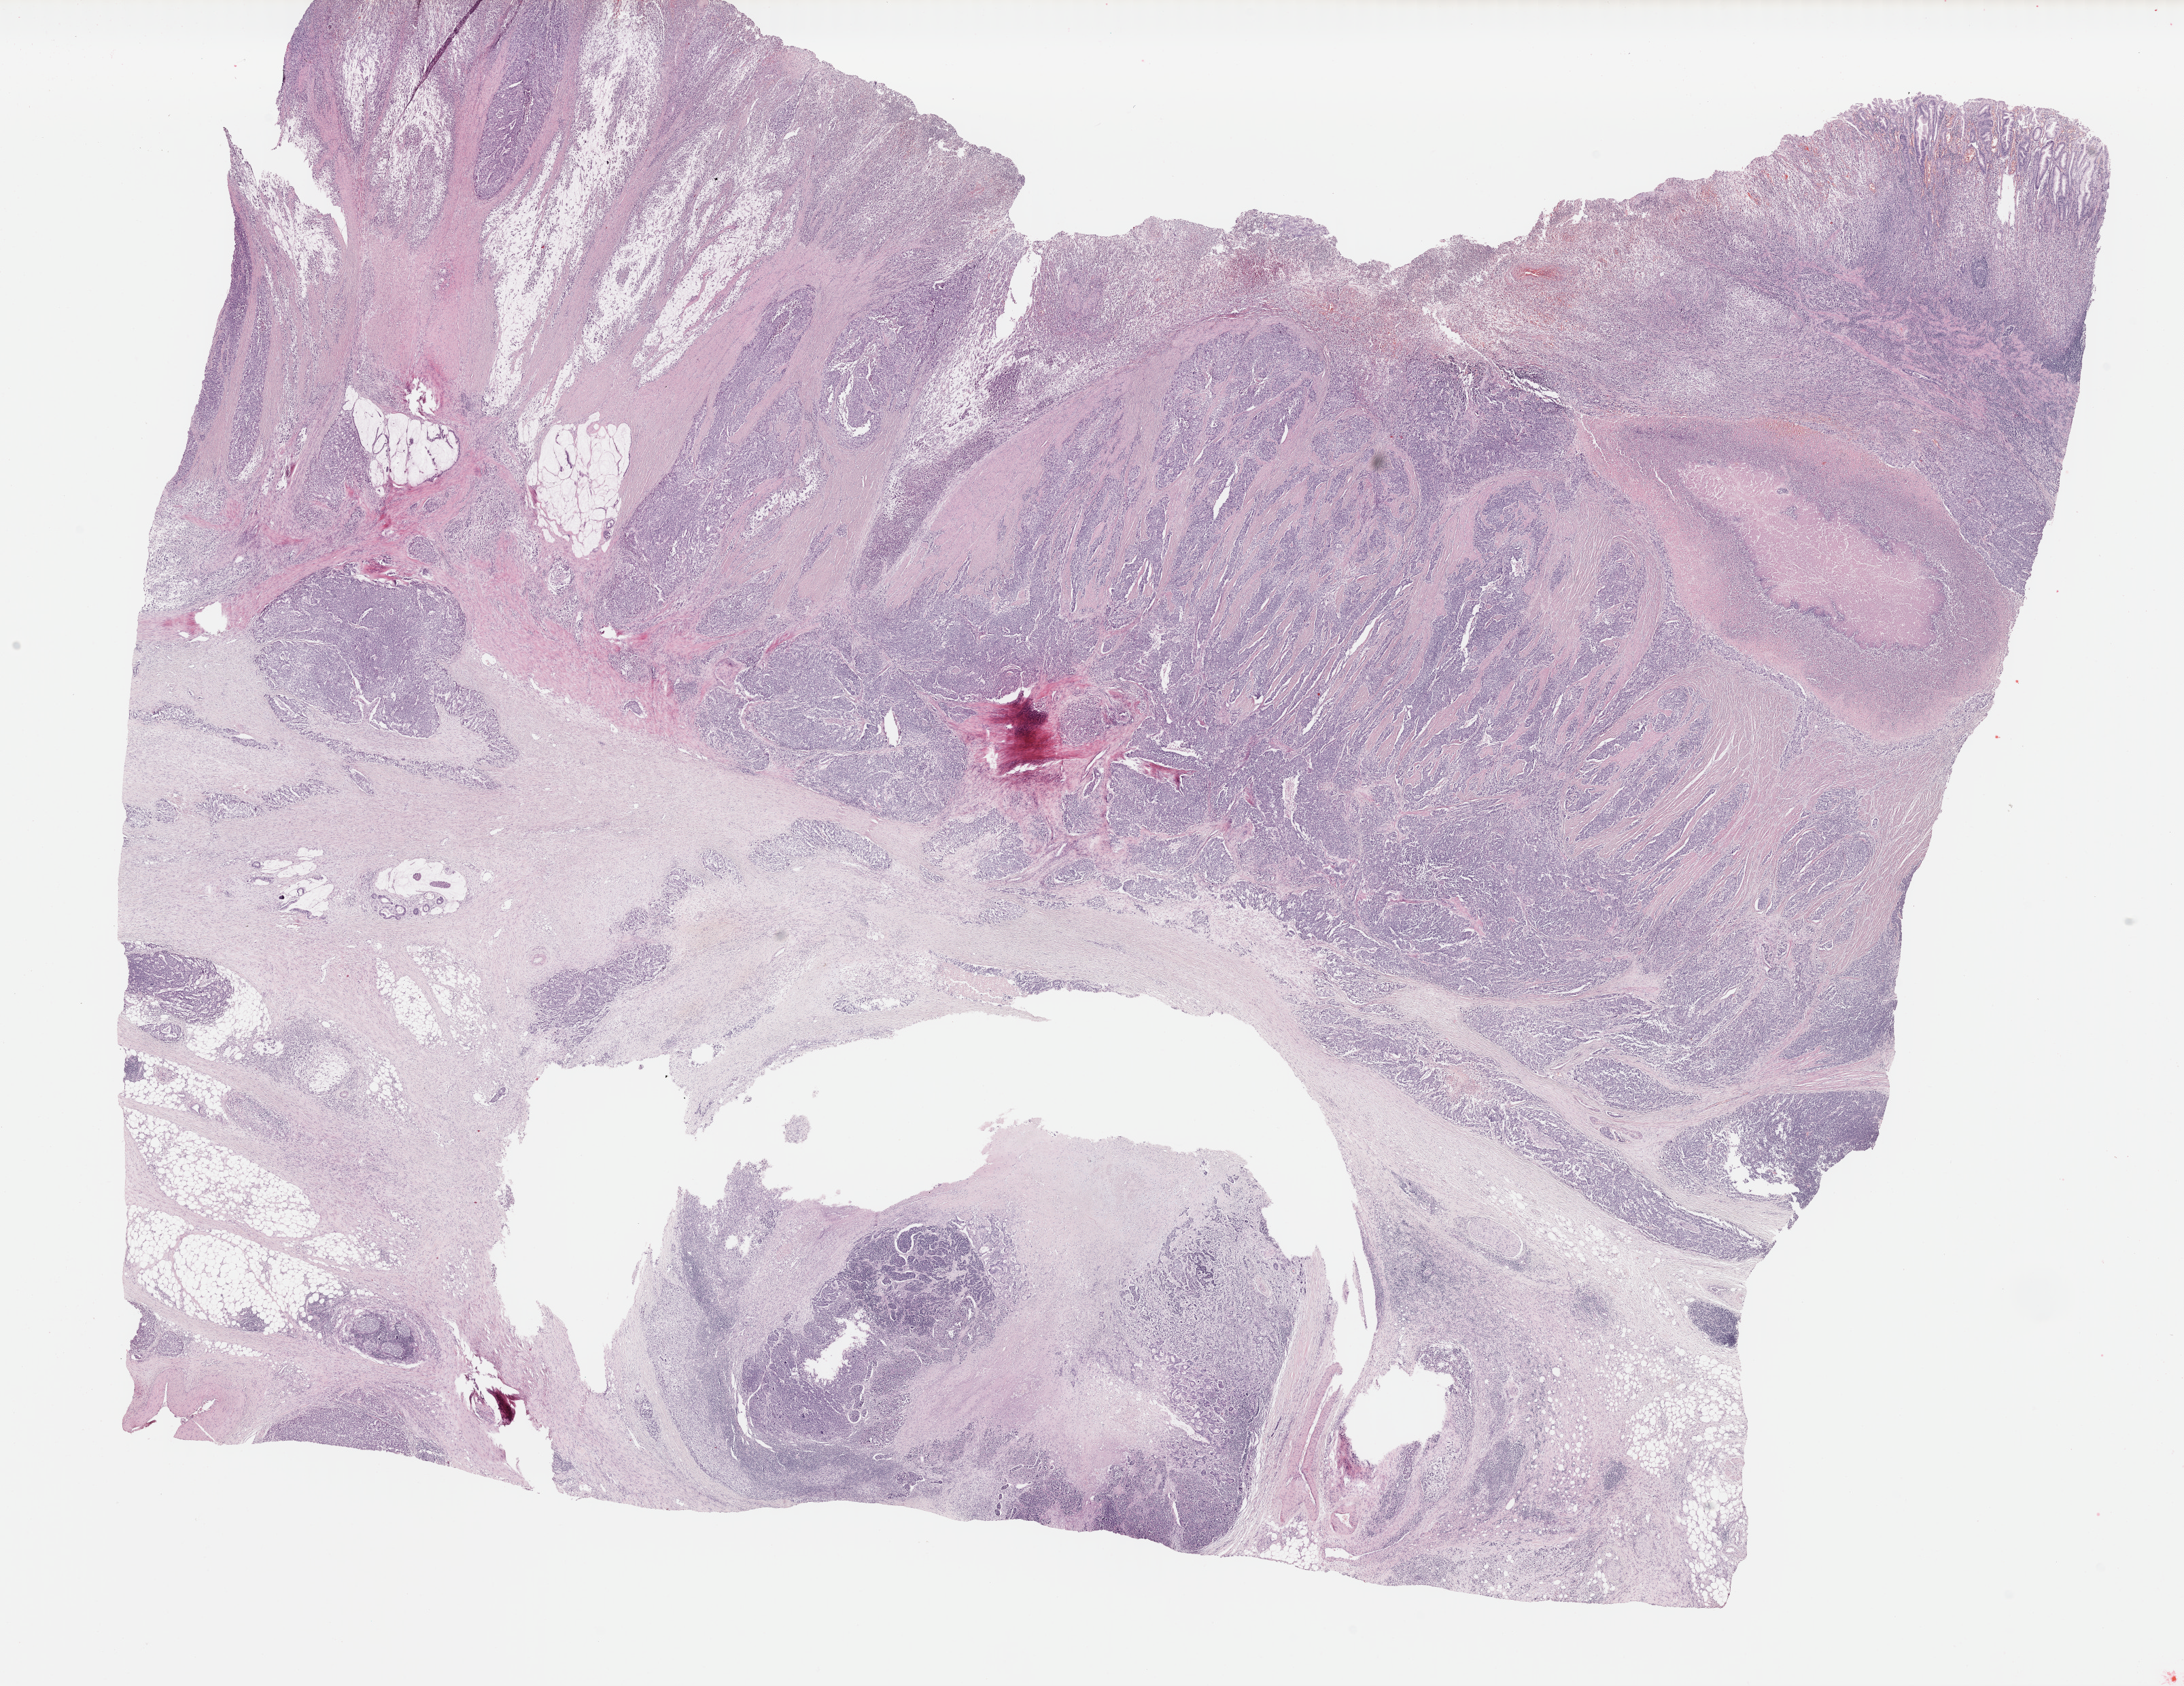
Whole-slide histology image, H&E — shown as a low-resolution overview of the whole scanned area (about 25.3 x 19.5 mm, slide scanned at 40x); formalin-fixed paraffin-embedded (FFPE) diagnostic section; primary tumour sample from the stomach. Male, age 53 years at initial diagnosis. Histologic grade: G3 (poorly differentiated).
* diagnosis: Carcinoma, diffuse type (body of stomach)
* AJCC pathologic stage: IIIA (7th edition)
* lymph nodes positive (case pathology): 11 of 22 examined